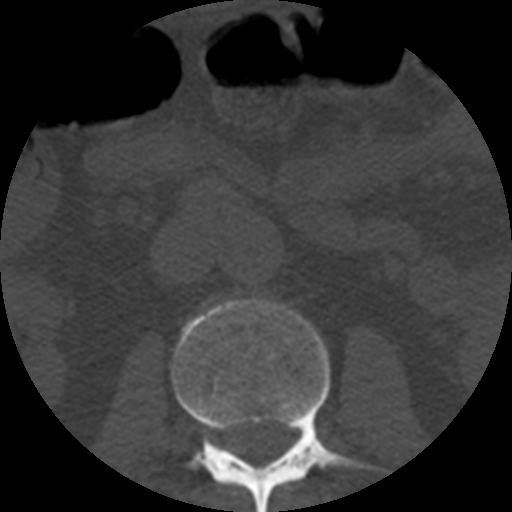
CT including the spine, one axial slice; slice 149 of 508 in the series (ordered by position); reconstruction kernel STANDARD; bone window (W 1800 / L 400 HU); 512 × 512 image matrix, field of view 160 × 160 mm. Patient age 57 years. Case-level facts recorded for this patient, not image findings: primary cancer: prostate.
Structures marked on this image (semi-automatically segmented with operator editing):
- L2 vertebra: box from (x=171, y=300) to (x=373, y=512) px